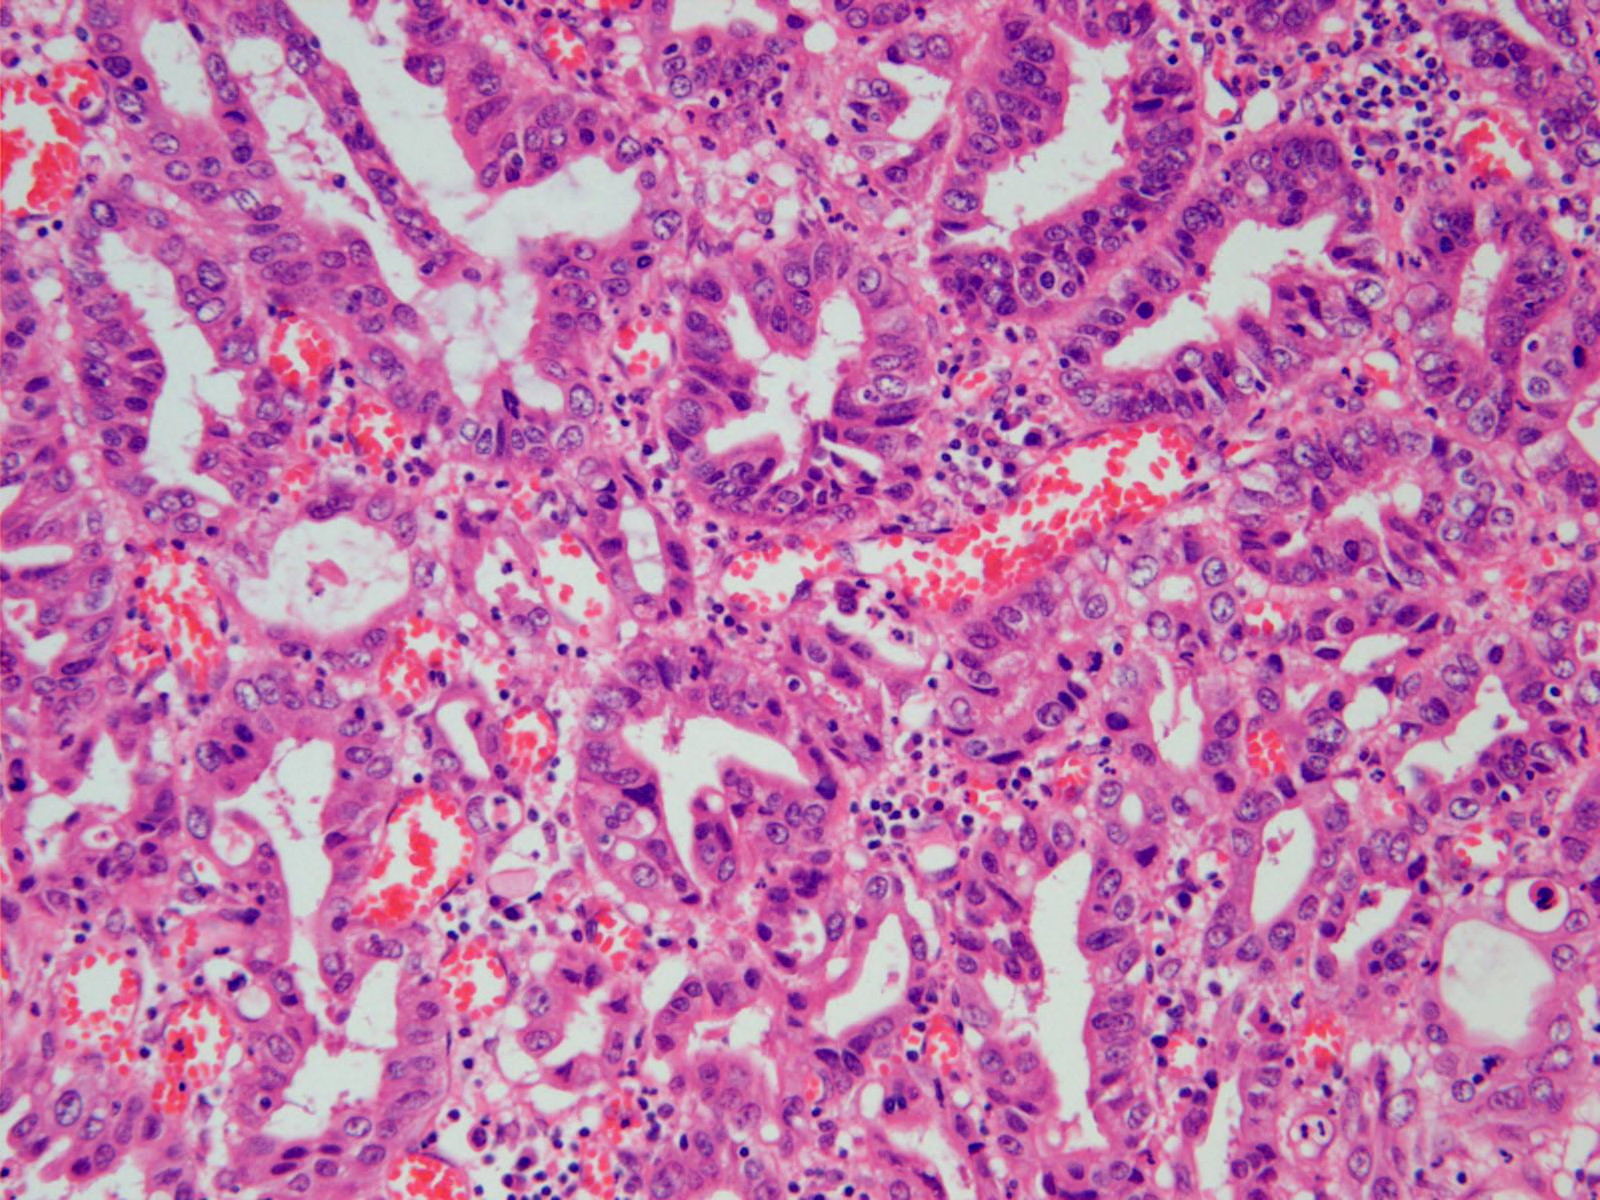
H&E-stained micrograph of a single small tissue field — roughly 0.8 x 0.6 mm in extent; formalin-fixed paraffin-embedded (FFPE) diagnostic section; primary tumour sample from the stomach. Male patient; age at initial diagnosis 70 years. Histologic grade: G2 (moderately differentiated).
Histologic diagnosis: Adenocarcinoma, NOS (gastric antrum). Lymph nodes positive (case pathology): 1 of 8 examined. AJCC pathologic stage: IIIA (6th edition).